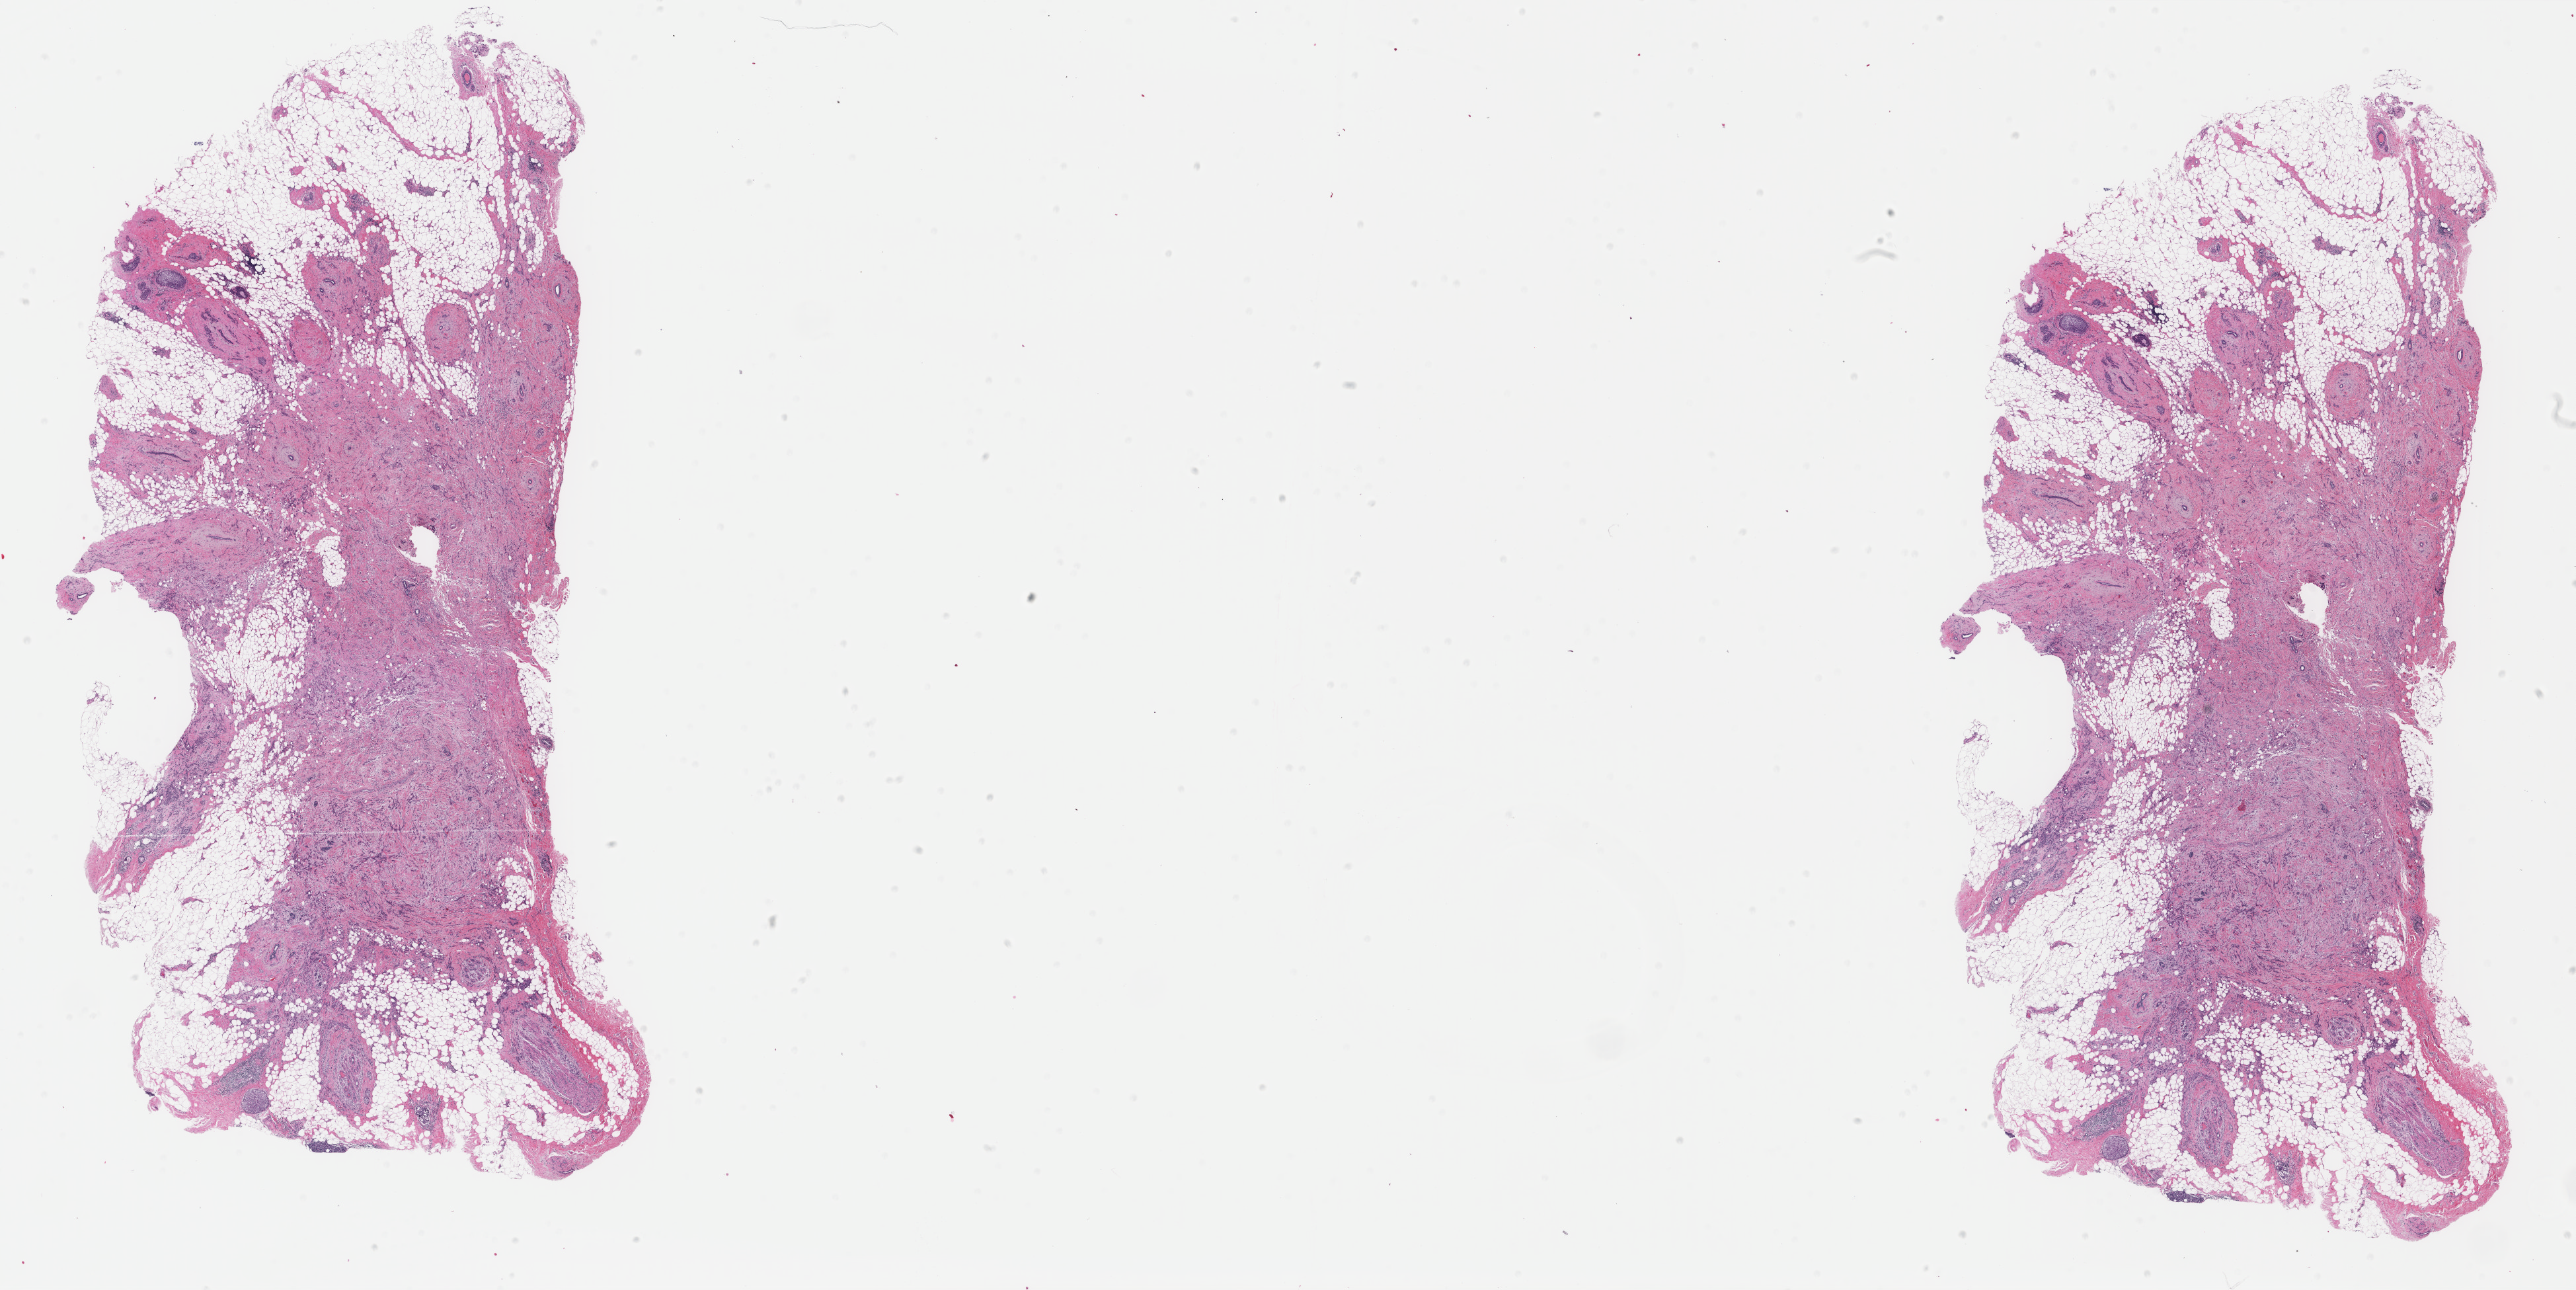
Whole-slide histology image, Hematoxylin and eosin (H&E) stained, low-resolution overview of the scanned area, about 30.9 x 15.5 mm (acquisition: 40x scan); FFPE section; primary tumour sample from the breast. Female, age 61 years at initial diagnosis.
* laterality: right
* histologic diagnosis: Infiltrating duct carcinoma, NOS
* AJCC pathologic stage: IA
* lymph nodes positive (case pathology): 0 of 10 examined